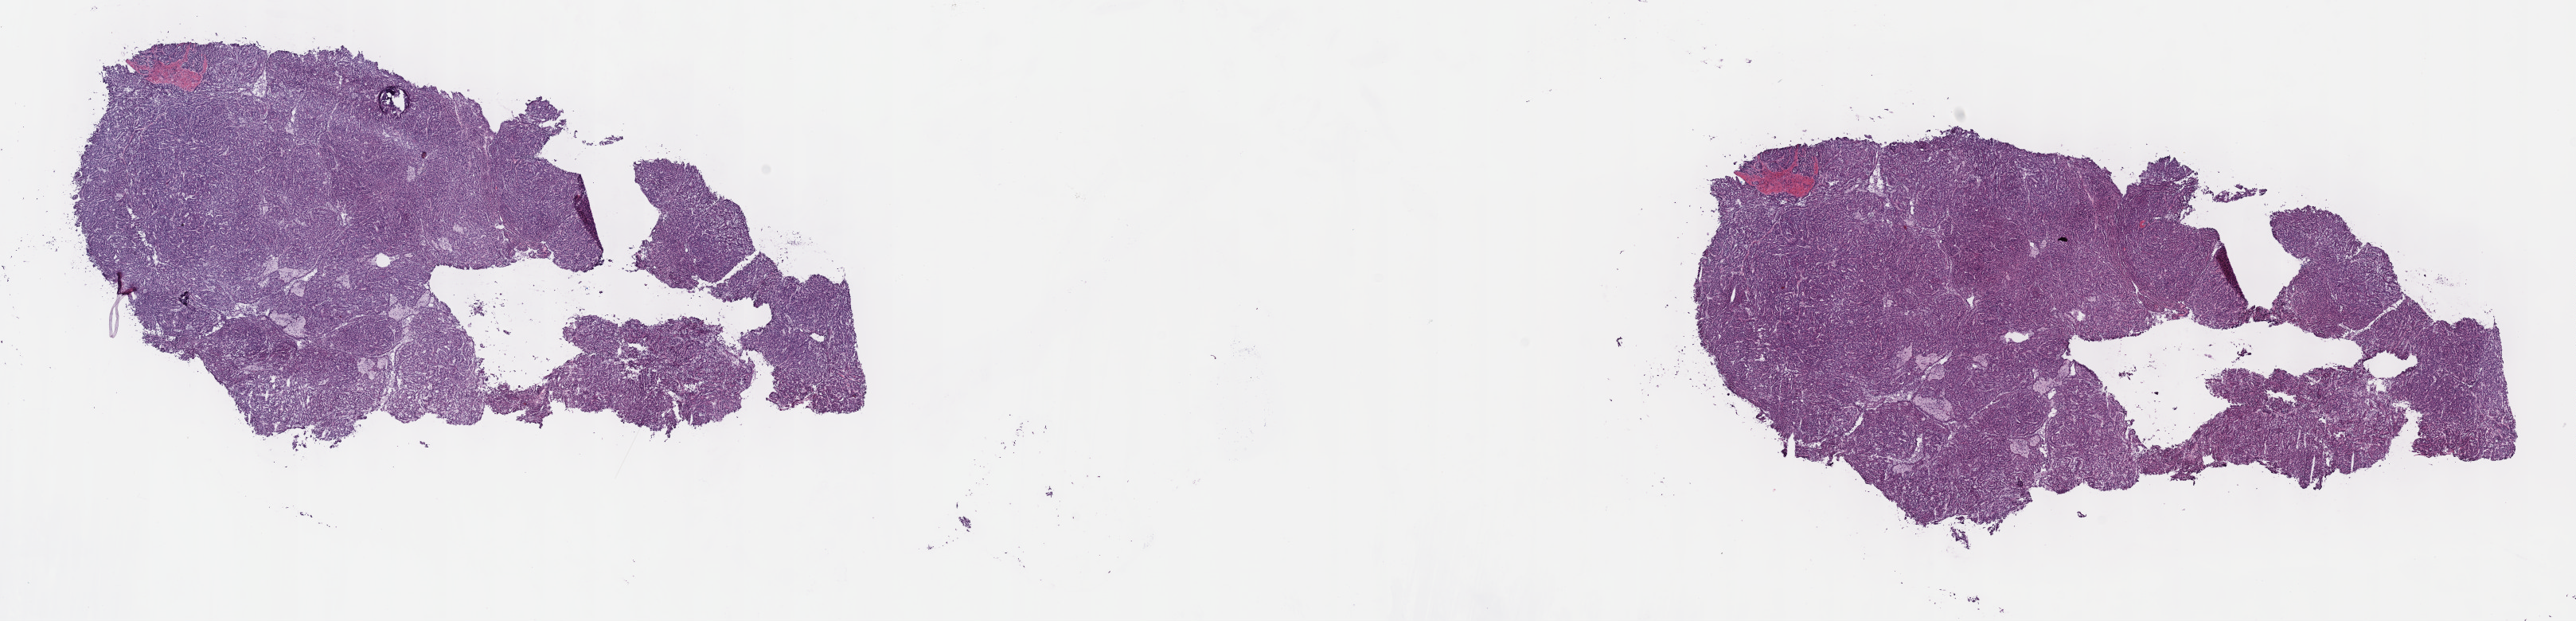
Digitized Hematoxylin and eosin (H&E) stained tissue section (whole slide), a low-resolution overview of the entire scanned area, about 26.2 x 6.3 mm; frozen section from the top of the tissue portion; primary tumour sample from the kidney. Patient: male, age at initial diagnosis 58 years. Composition of this section per pathologist review: tumour cells 94%, tumour nuclei 95%, normal cells 0%, stromal cells 5%, necrosis 1%. Inflammatory infiltration, as recorded: lymphocyte infiltration 2%, monocyte infiltration 3%, neutrophil infiltration 0%.
• laterality: left
• TNM: T1a NX MX
• diagnosis: Papillary adenocarcinoma, NOS
• AJCC pathologic stage: I (7th edition)